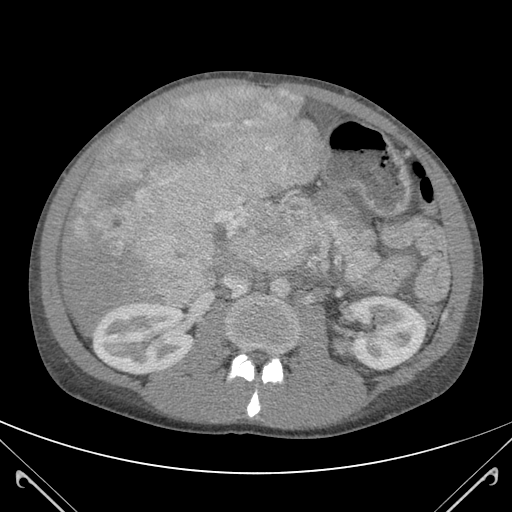
Contrast-enhanced abdominal CT (liver protocol), one axial slice. Slice 56 of 118 in the series (ordered by position). Soft-tissue window (W 400 / L 40 HU). 3 mm slice thickness. 512 × 512 image matrix, field of view 380 × 380 mm. Case-level facts recorded for this patient, not image findings: diagnosis: hepatocellular carcinoma (patient treated with transarterial chemoembolisation; whether this scan precedes or follows treatment is not stated here); TNM stage (as recorded): Stage-IIIB.
Outlined on this slice (semi-automatically segmented with operator editing):
- abdominal aorta: bounding box <270,278,290,298> (left, top, right, bottom; pixels)
- liver parenchyma outside the tumour (the mass and vessels are separate outlines, so this box may not span the whole liver): <59,86,324,328>
- mass: <71,88,322,308>
- liver vessels: <183,98,297,299>